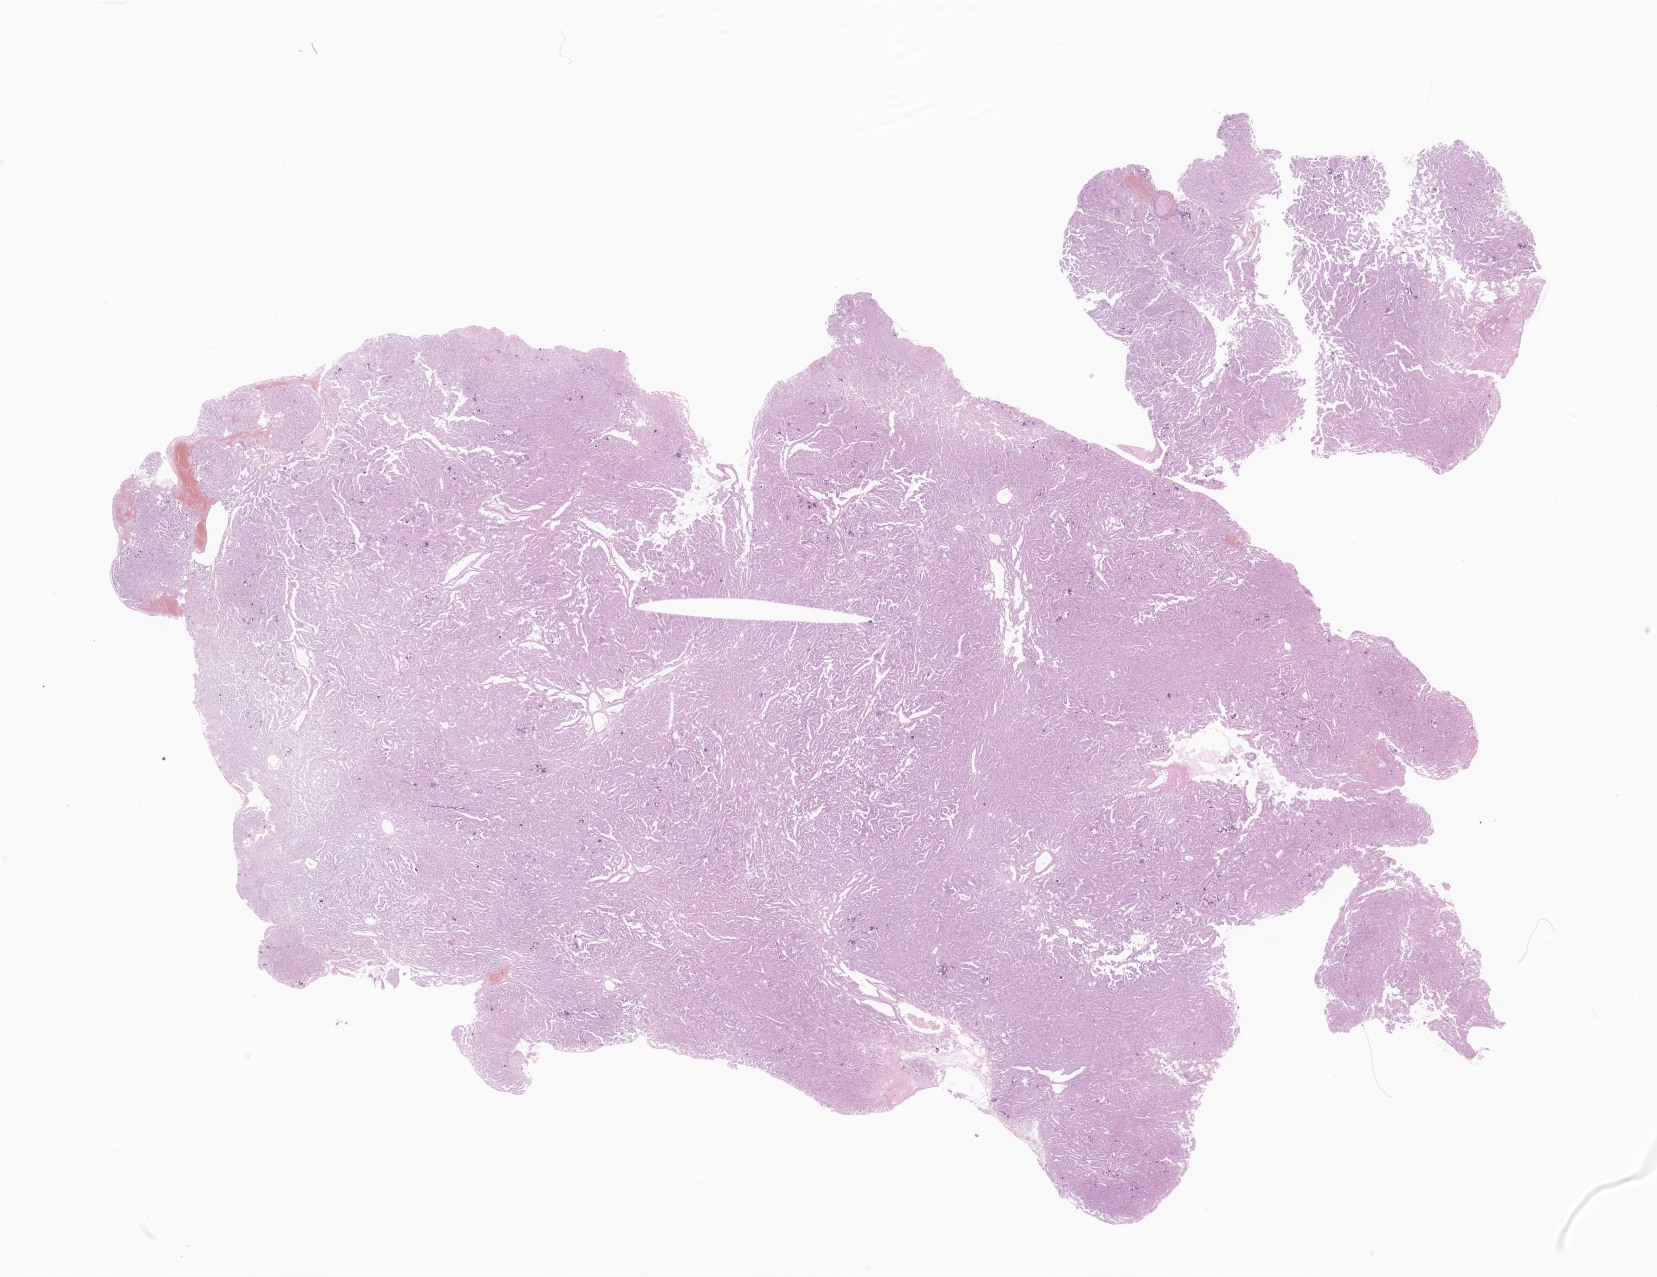
Whole-slide image, hematoxylin and eosin (H&E) stain of tumor tissue from the brain — low-resolution overview of the scanned area, about 28.0 x 21.5 mm, formalin-fixed, paraffin-embedded (FFPE) tissue. Patient female; age 119 months (9 years 11 months).
Diagnosis: Neoplasm, uncertain whether benign or malignant.